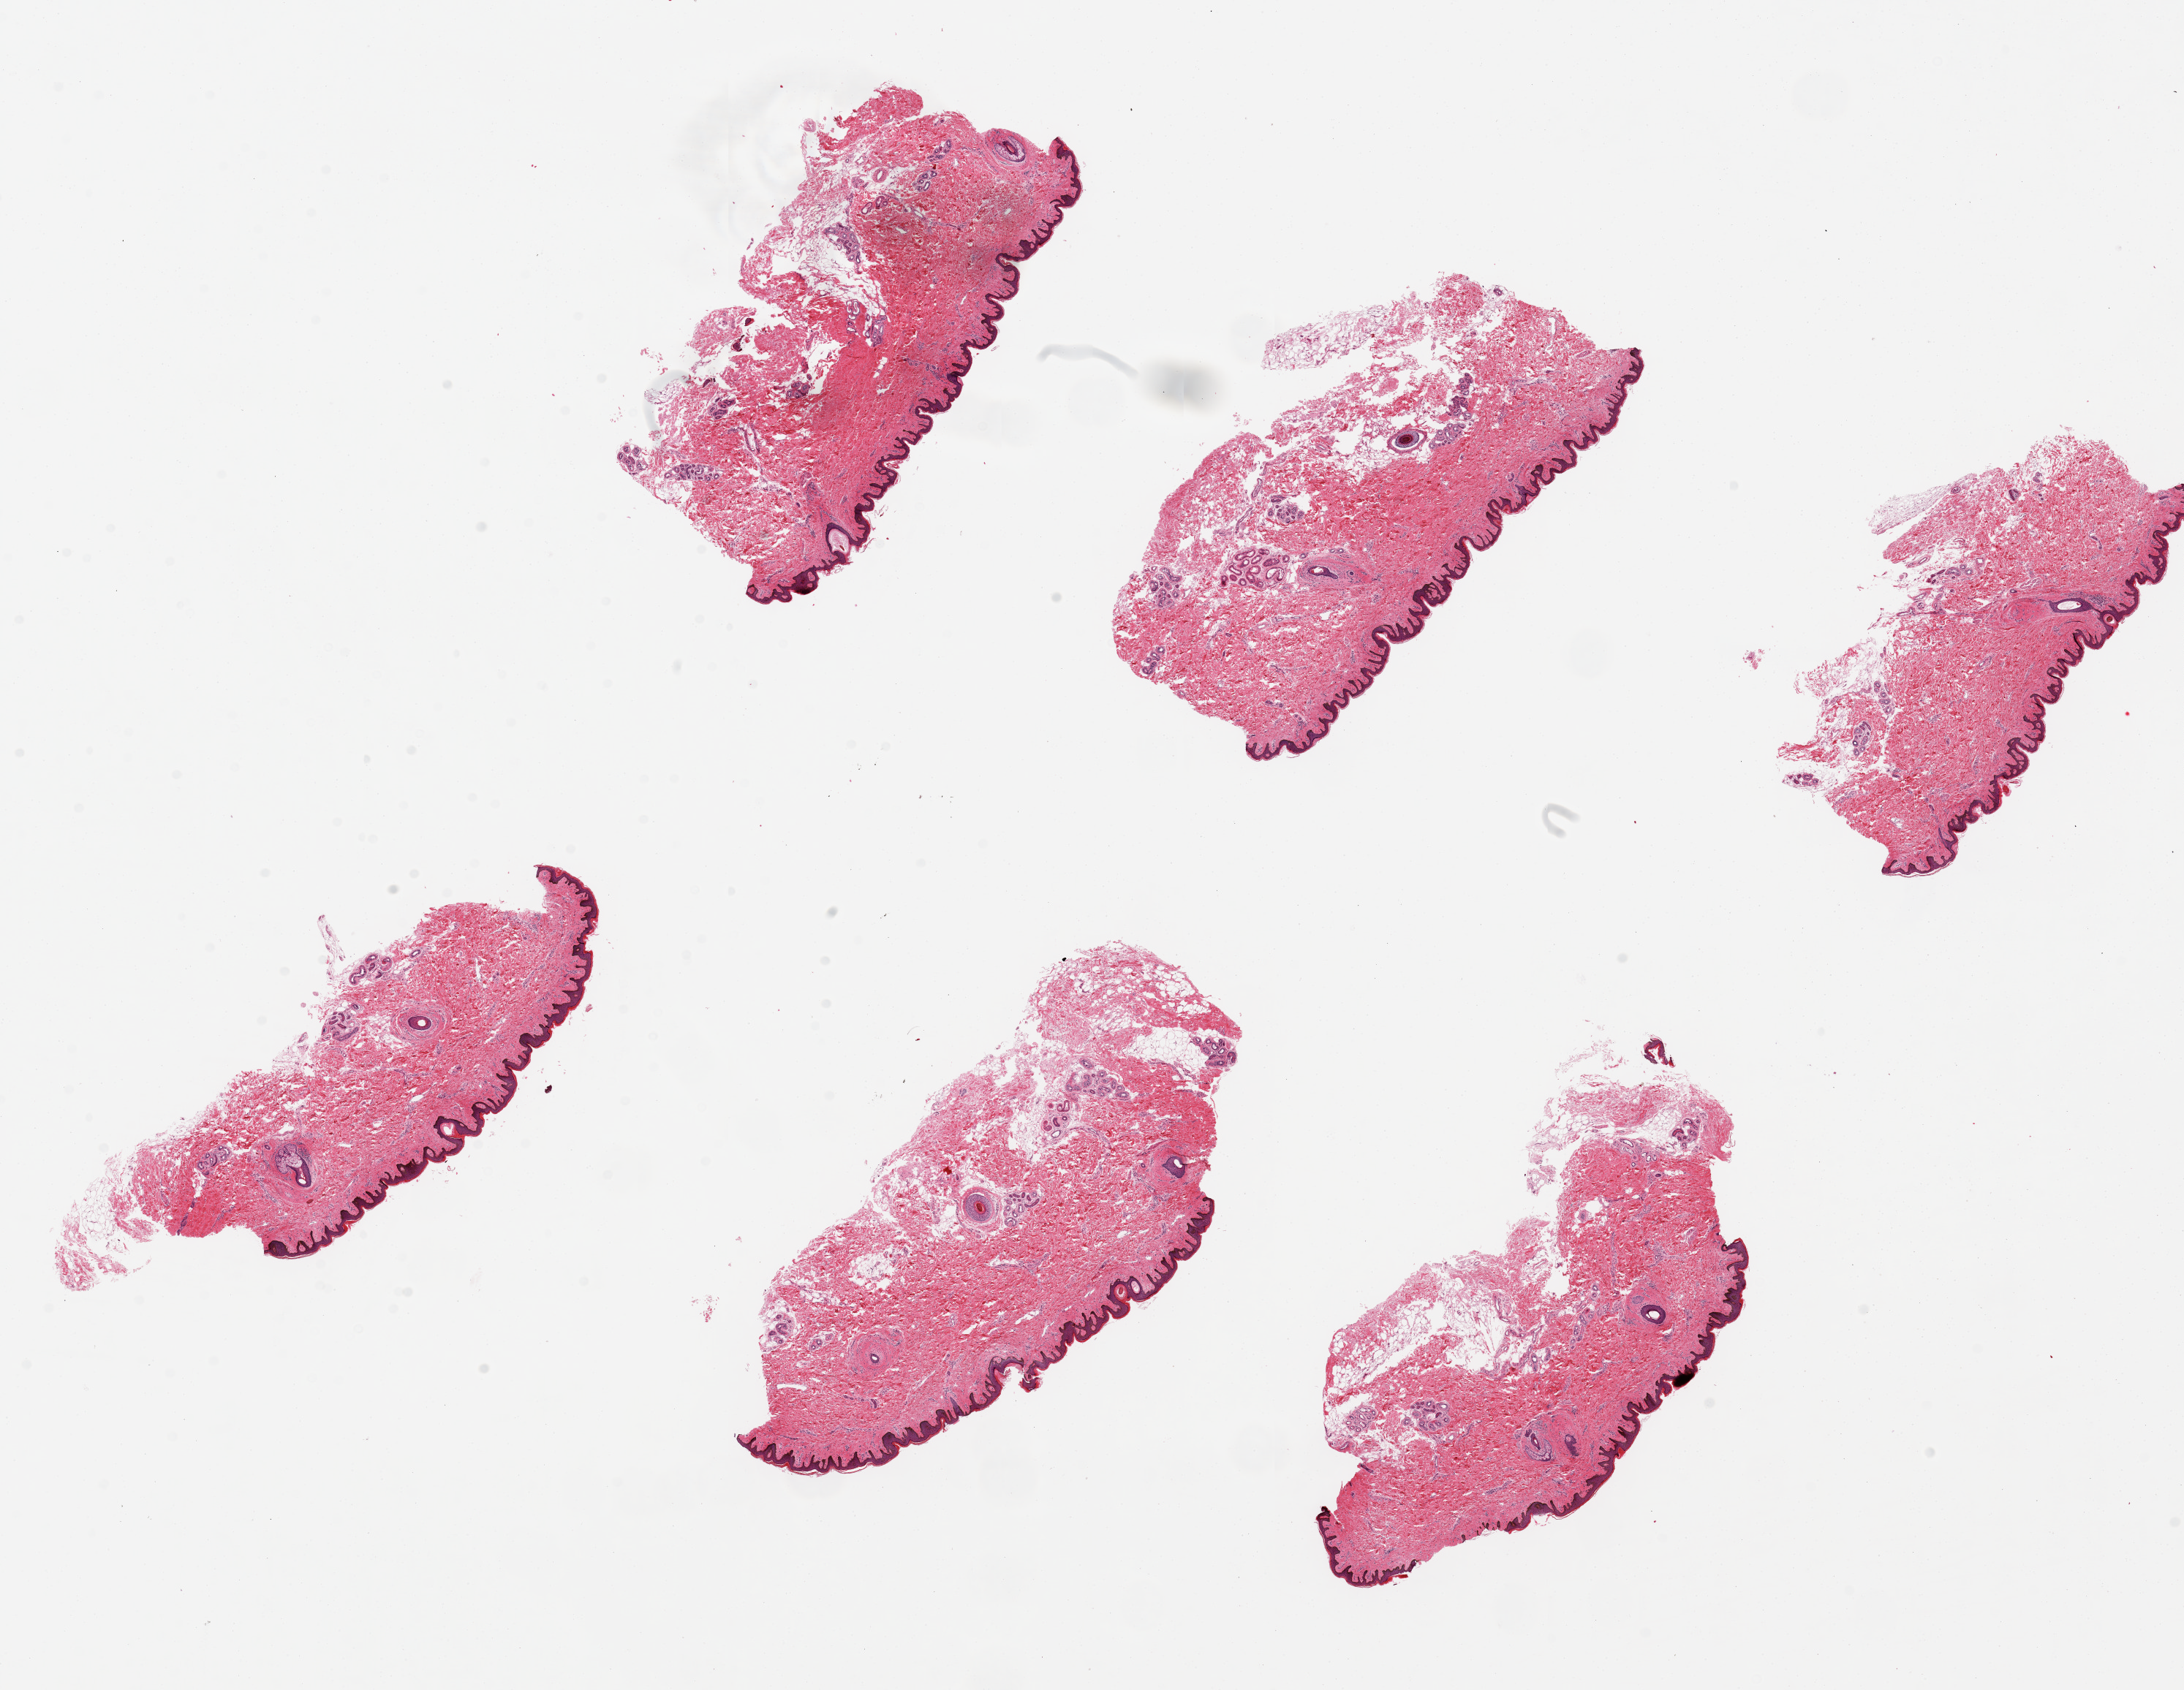
Whole-slide image, hematoxylin and eosin (H&E) stain, brightfield, shown as a low-resolution overview of the whole scanned area (about 23.6 x 18.3 mm), PAXgene-fixed, paraffin-embedded tissue, section of skin of suprapubic region (target tissue), donor tissue sample. Female donor.
* review note (as recorded): 6 pieces, up to 7x3.5mm; squamous epithelium is ~2.5% thickness